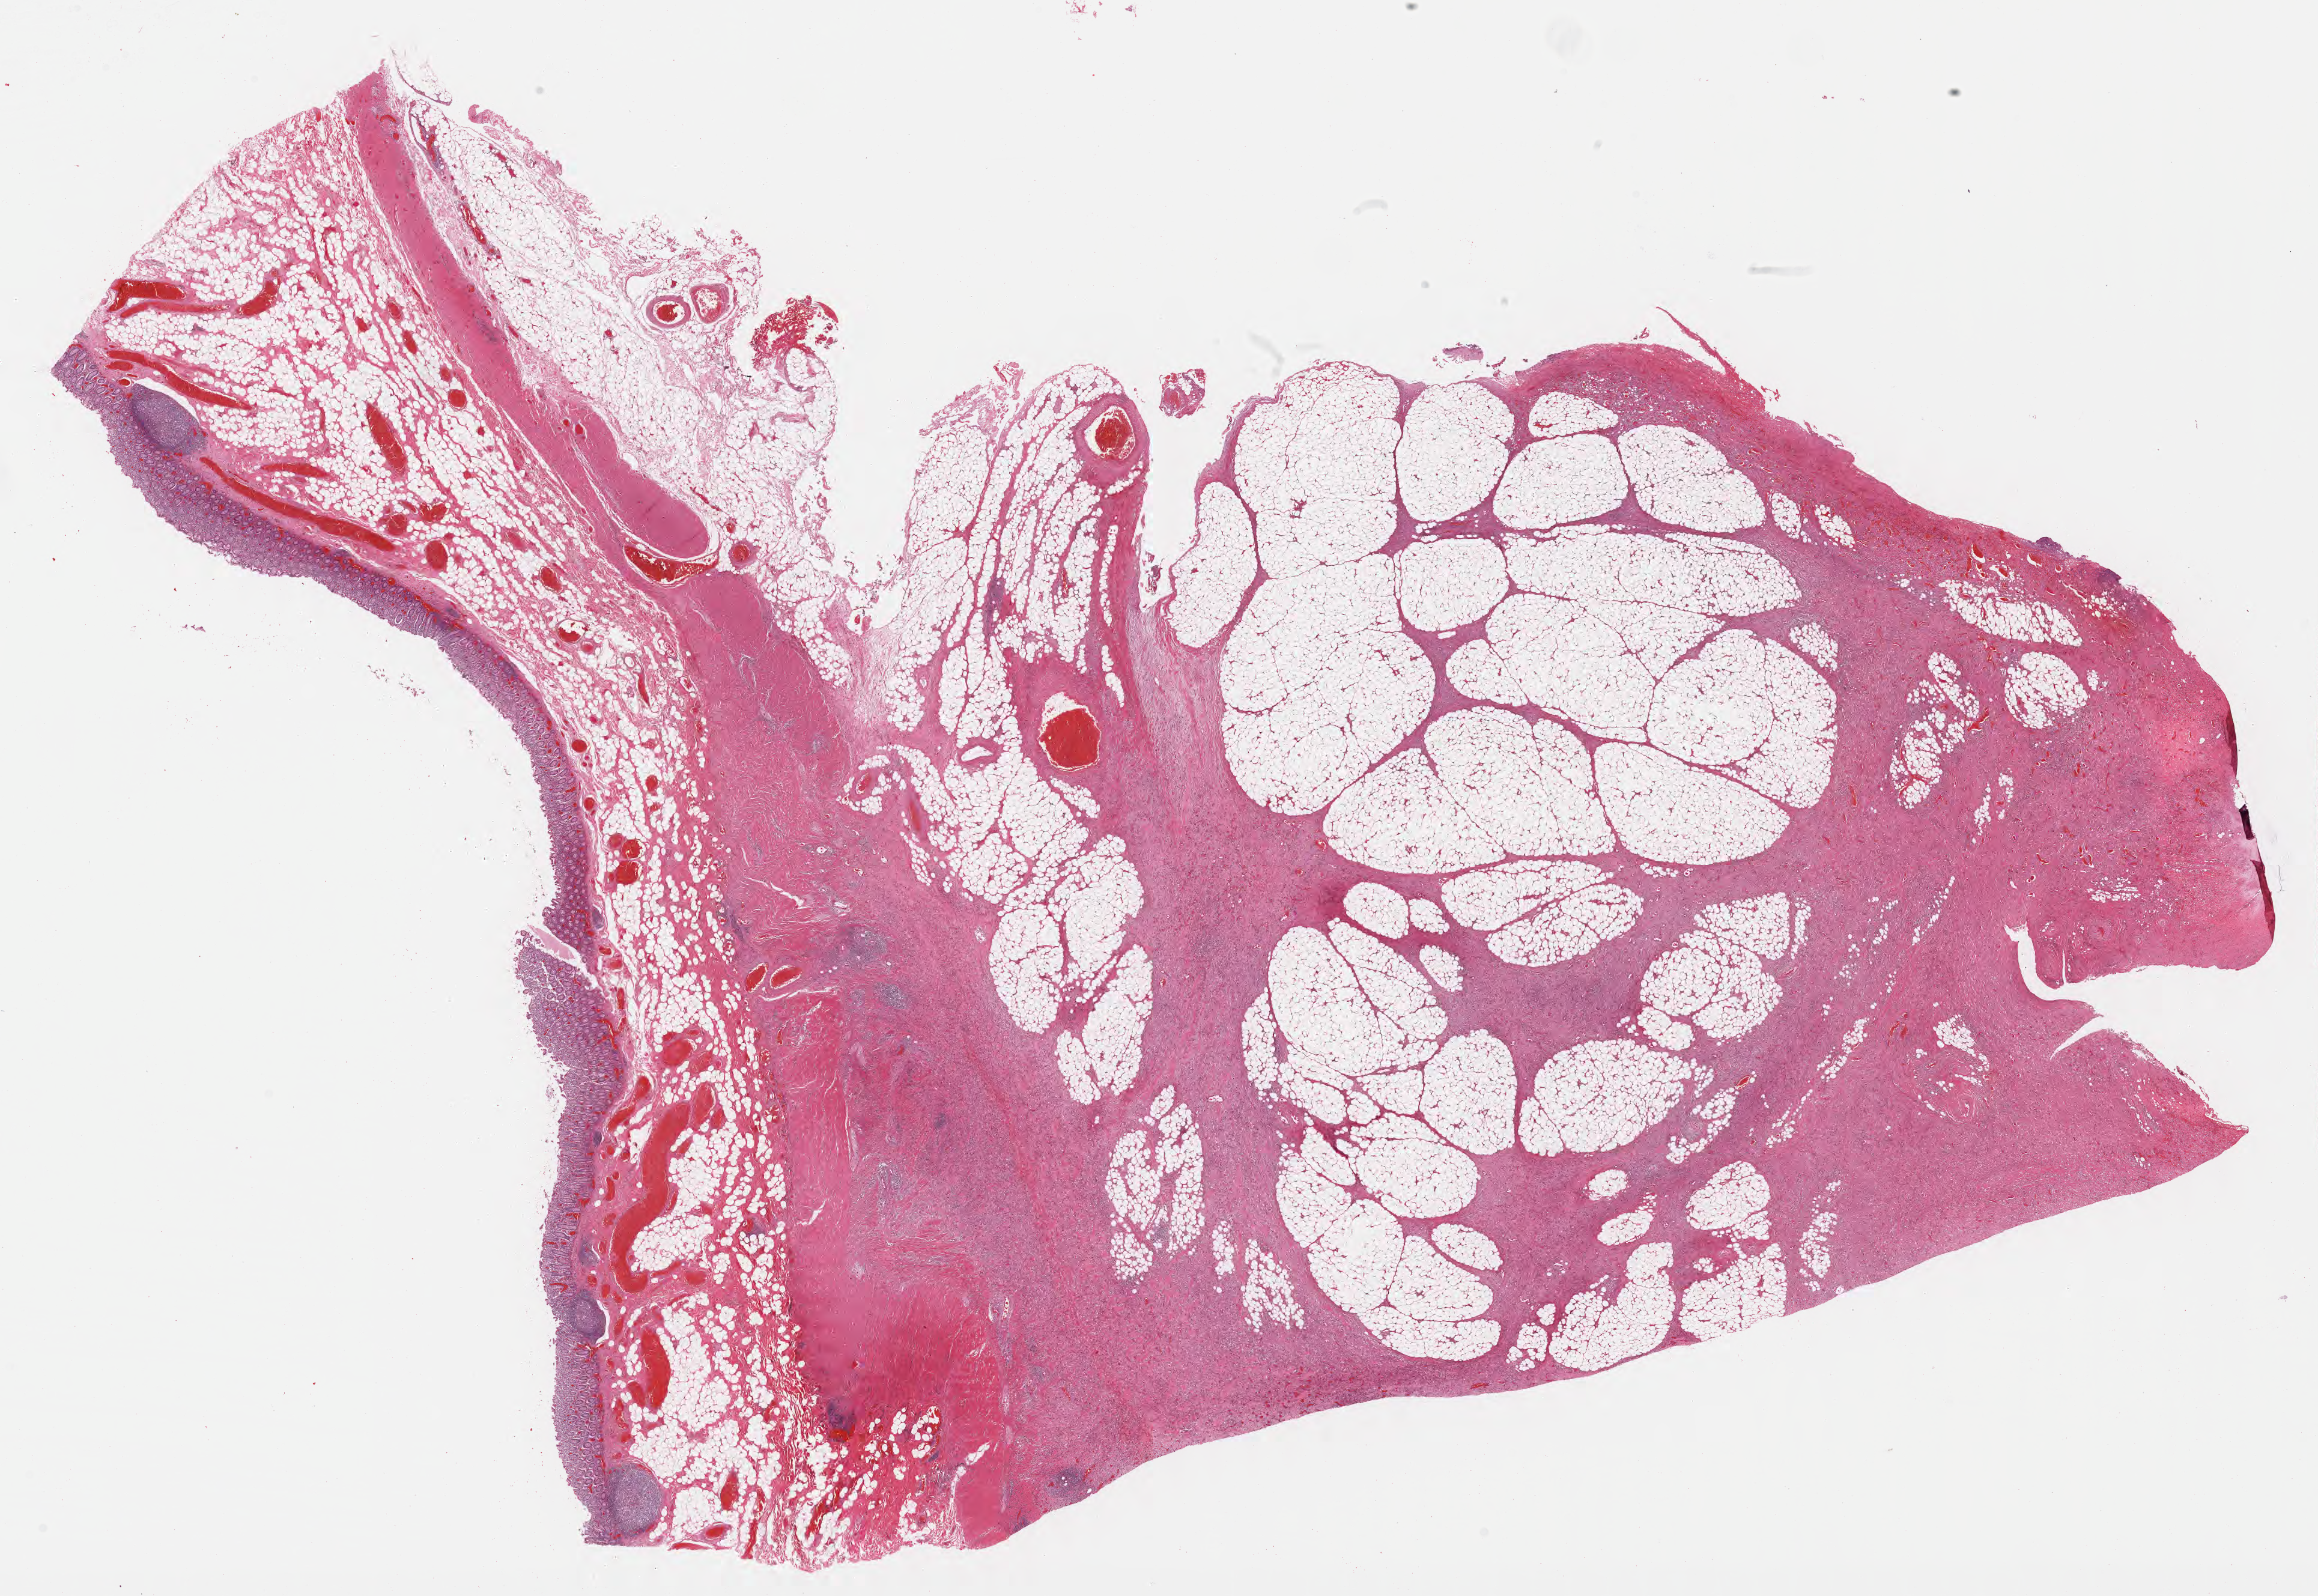
H&E whole-slide image, a low-resolution overview of the entire scanned area, about 31.2 x 21.5 mm, formalin-fixed paraffin-embedded section, specimen: normal-tissue sample (non-tumor) from a patient with burkitt lymphoma, NOS. Patient: male, aged 26. Pathologist review of this section (percent, as recorded): tumor cells 0%, tumor nuclei 0%, stromal cells 0%, necrosis 0%, normal cells 100%. Inflammatory infiltration, as recorded: lymphocyte infiltration 20%, monocyte infiltration 25%, neutrophil infiltration 10%.
This section: non-tumor tissue sample; the patient's diagnosis is given above. Section: bottom of the tissue portion.